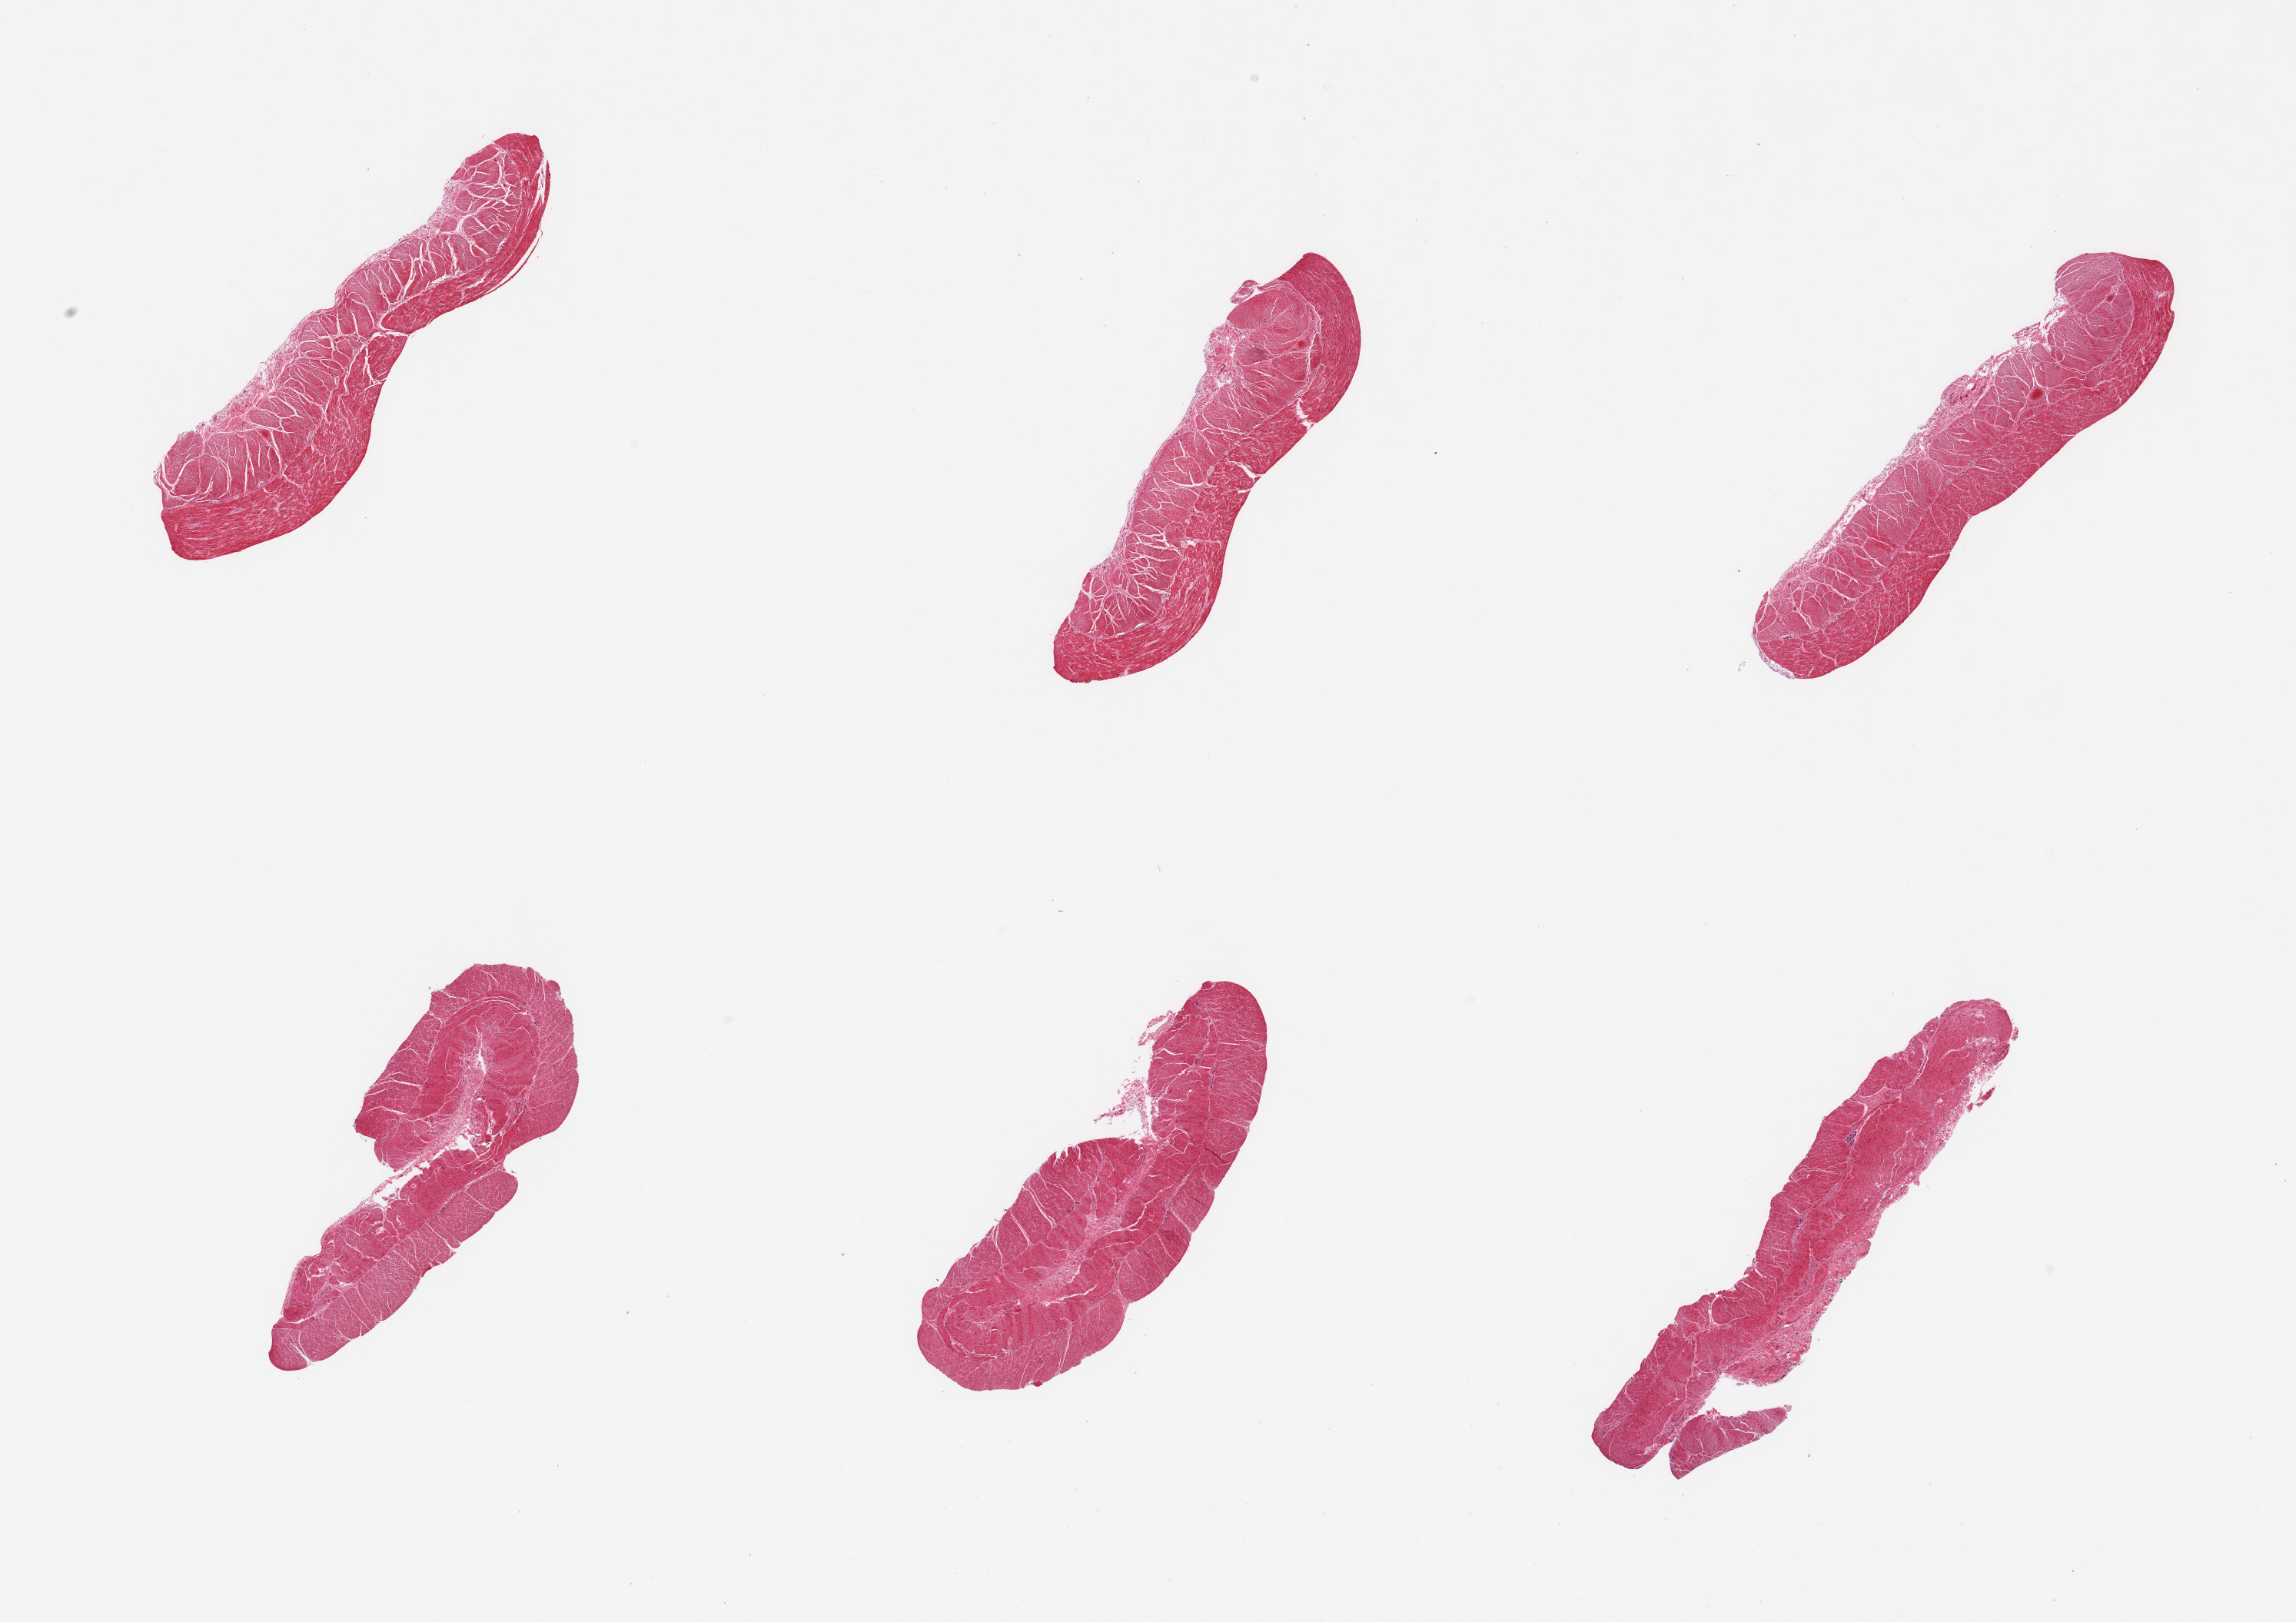
Digitized hematoxylin and eosin (H&E)-stained section, whole scanned area (about 23.6 x 16.7 mm, acquisition: 20x scan) shown as a low-resolution overview; PAXgene-fixed, paraffin-embedded tissue; sampled site (target tissue): sigmoid colon; tissue donor sample. Donor sex: male.
Reviewer comment on this tissue sample: 6 pieces; target muscularis.